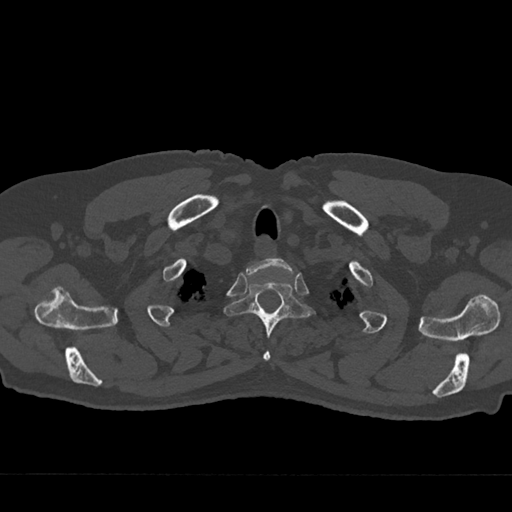
CT including the spine, one axial slice. Position 622 of 797 along the scan axis. Reconstruction kernel Br40s/3. 120 kVp. Bone window (W 1800 / L 400 HU). 0.5 mm slice thickness. 512 × 512 image matrix, field of view 377 × 377 mm. Patient: male, 75 years. From the clinical record (not read from this slice): primary cancer: renal; vertebrae with lytic lesions (as recorded): T4.
Annotated regions visible in this slice (semi-automatically segmented with operator editing):
- T1 vertebra: bounding box (x1, y1, x2, y2) in pixels: (246, 258, 294, 277)
- T2 vertebra: (224, 278, 314, 361)